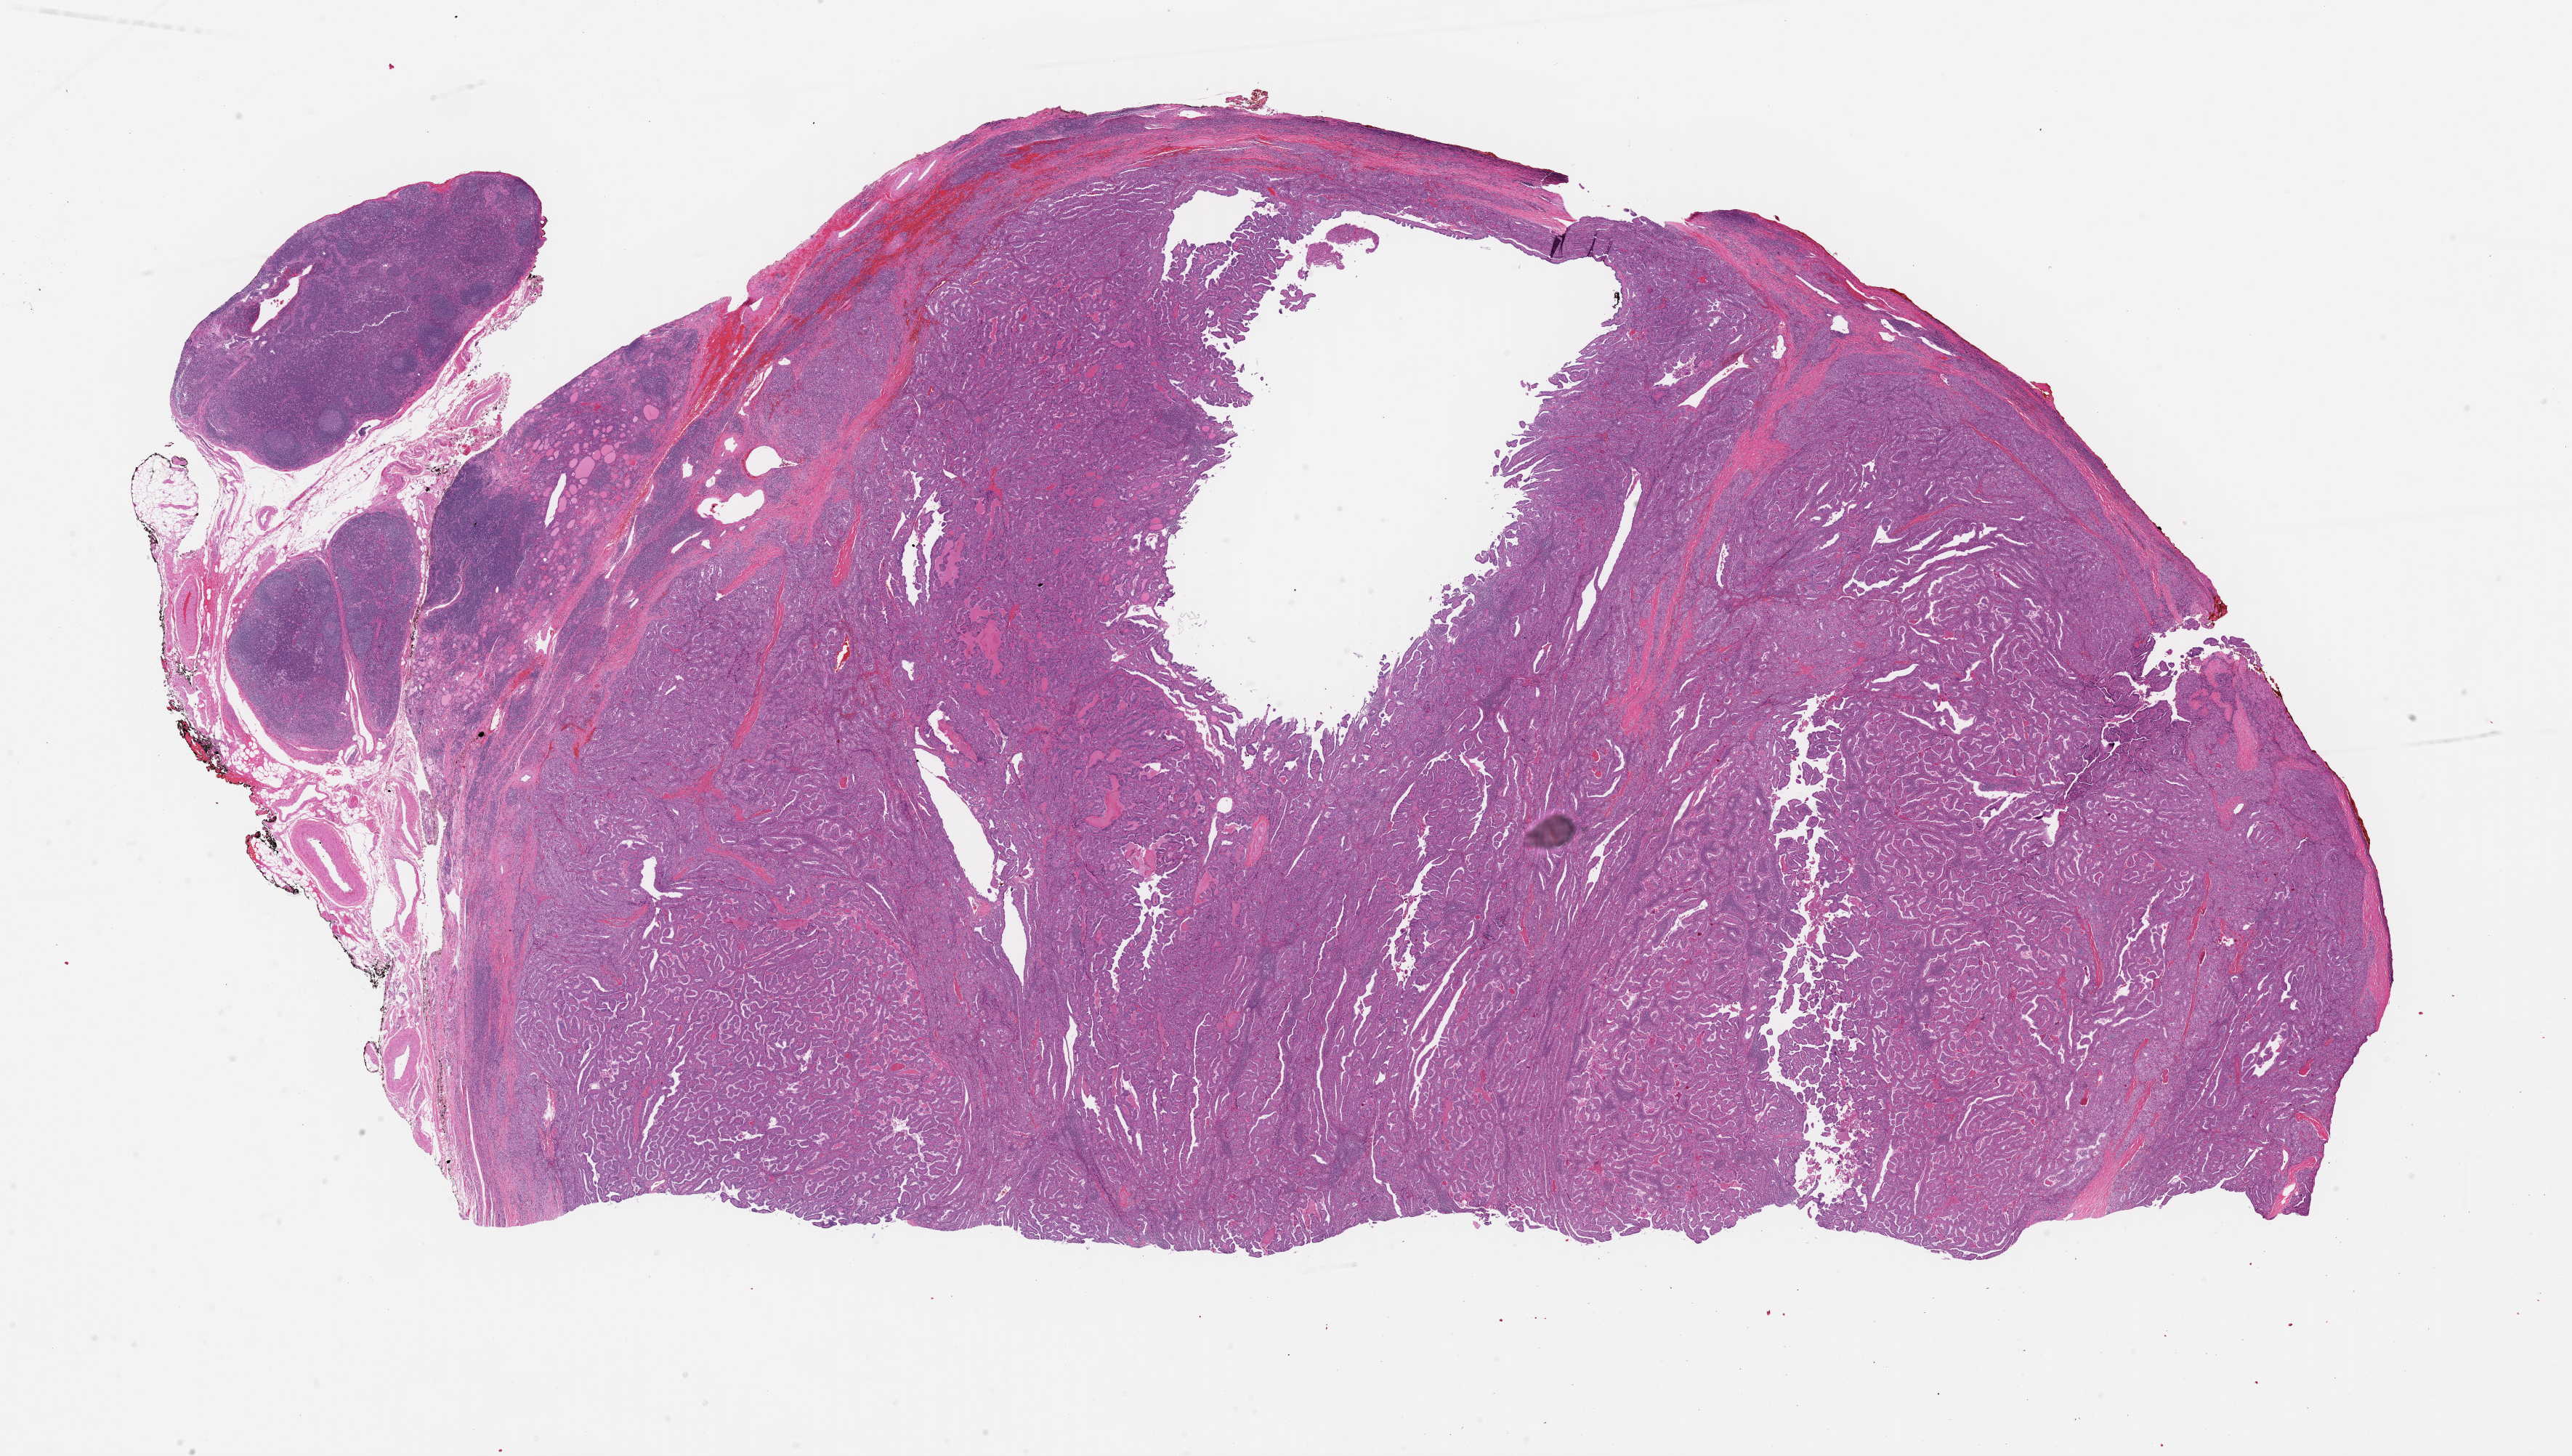
Hematoxylin and eosin (H&E) stained whole-slide image — shown as a low-resolution overview of the whole scanned area (about 28.0 x 15.8 mm). Formalin-fixed paraffin-embedded (FFPE) diagnostic section. Sample: primary tumour, thyroid. Patient: male, age at initial diagnosis 42 years.
Laterality: left. Lymph nodes positive (case pathology): 8 of 17 examined. Diagnosis: Papillary adenocarcinoma, NOS (thyroid gland). AJCC pathologic stage: I (7th edition). TNM: T3 N1a MX.